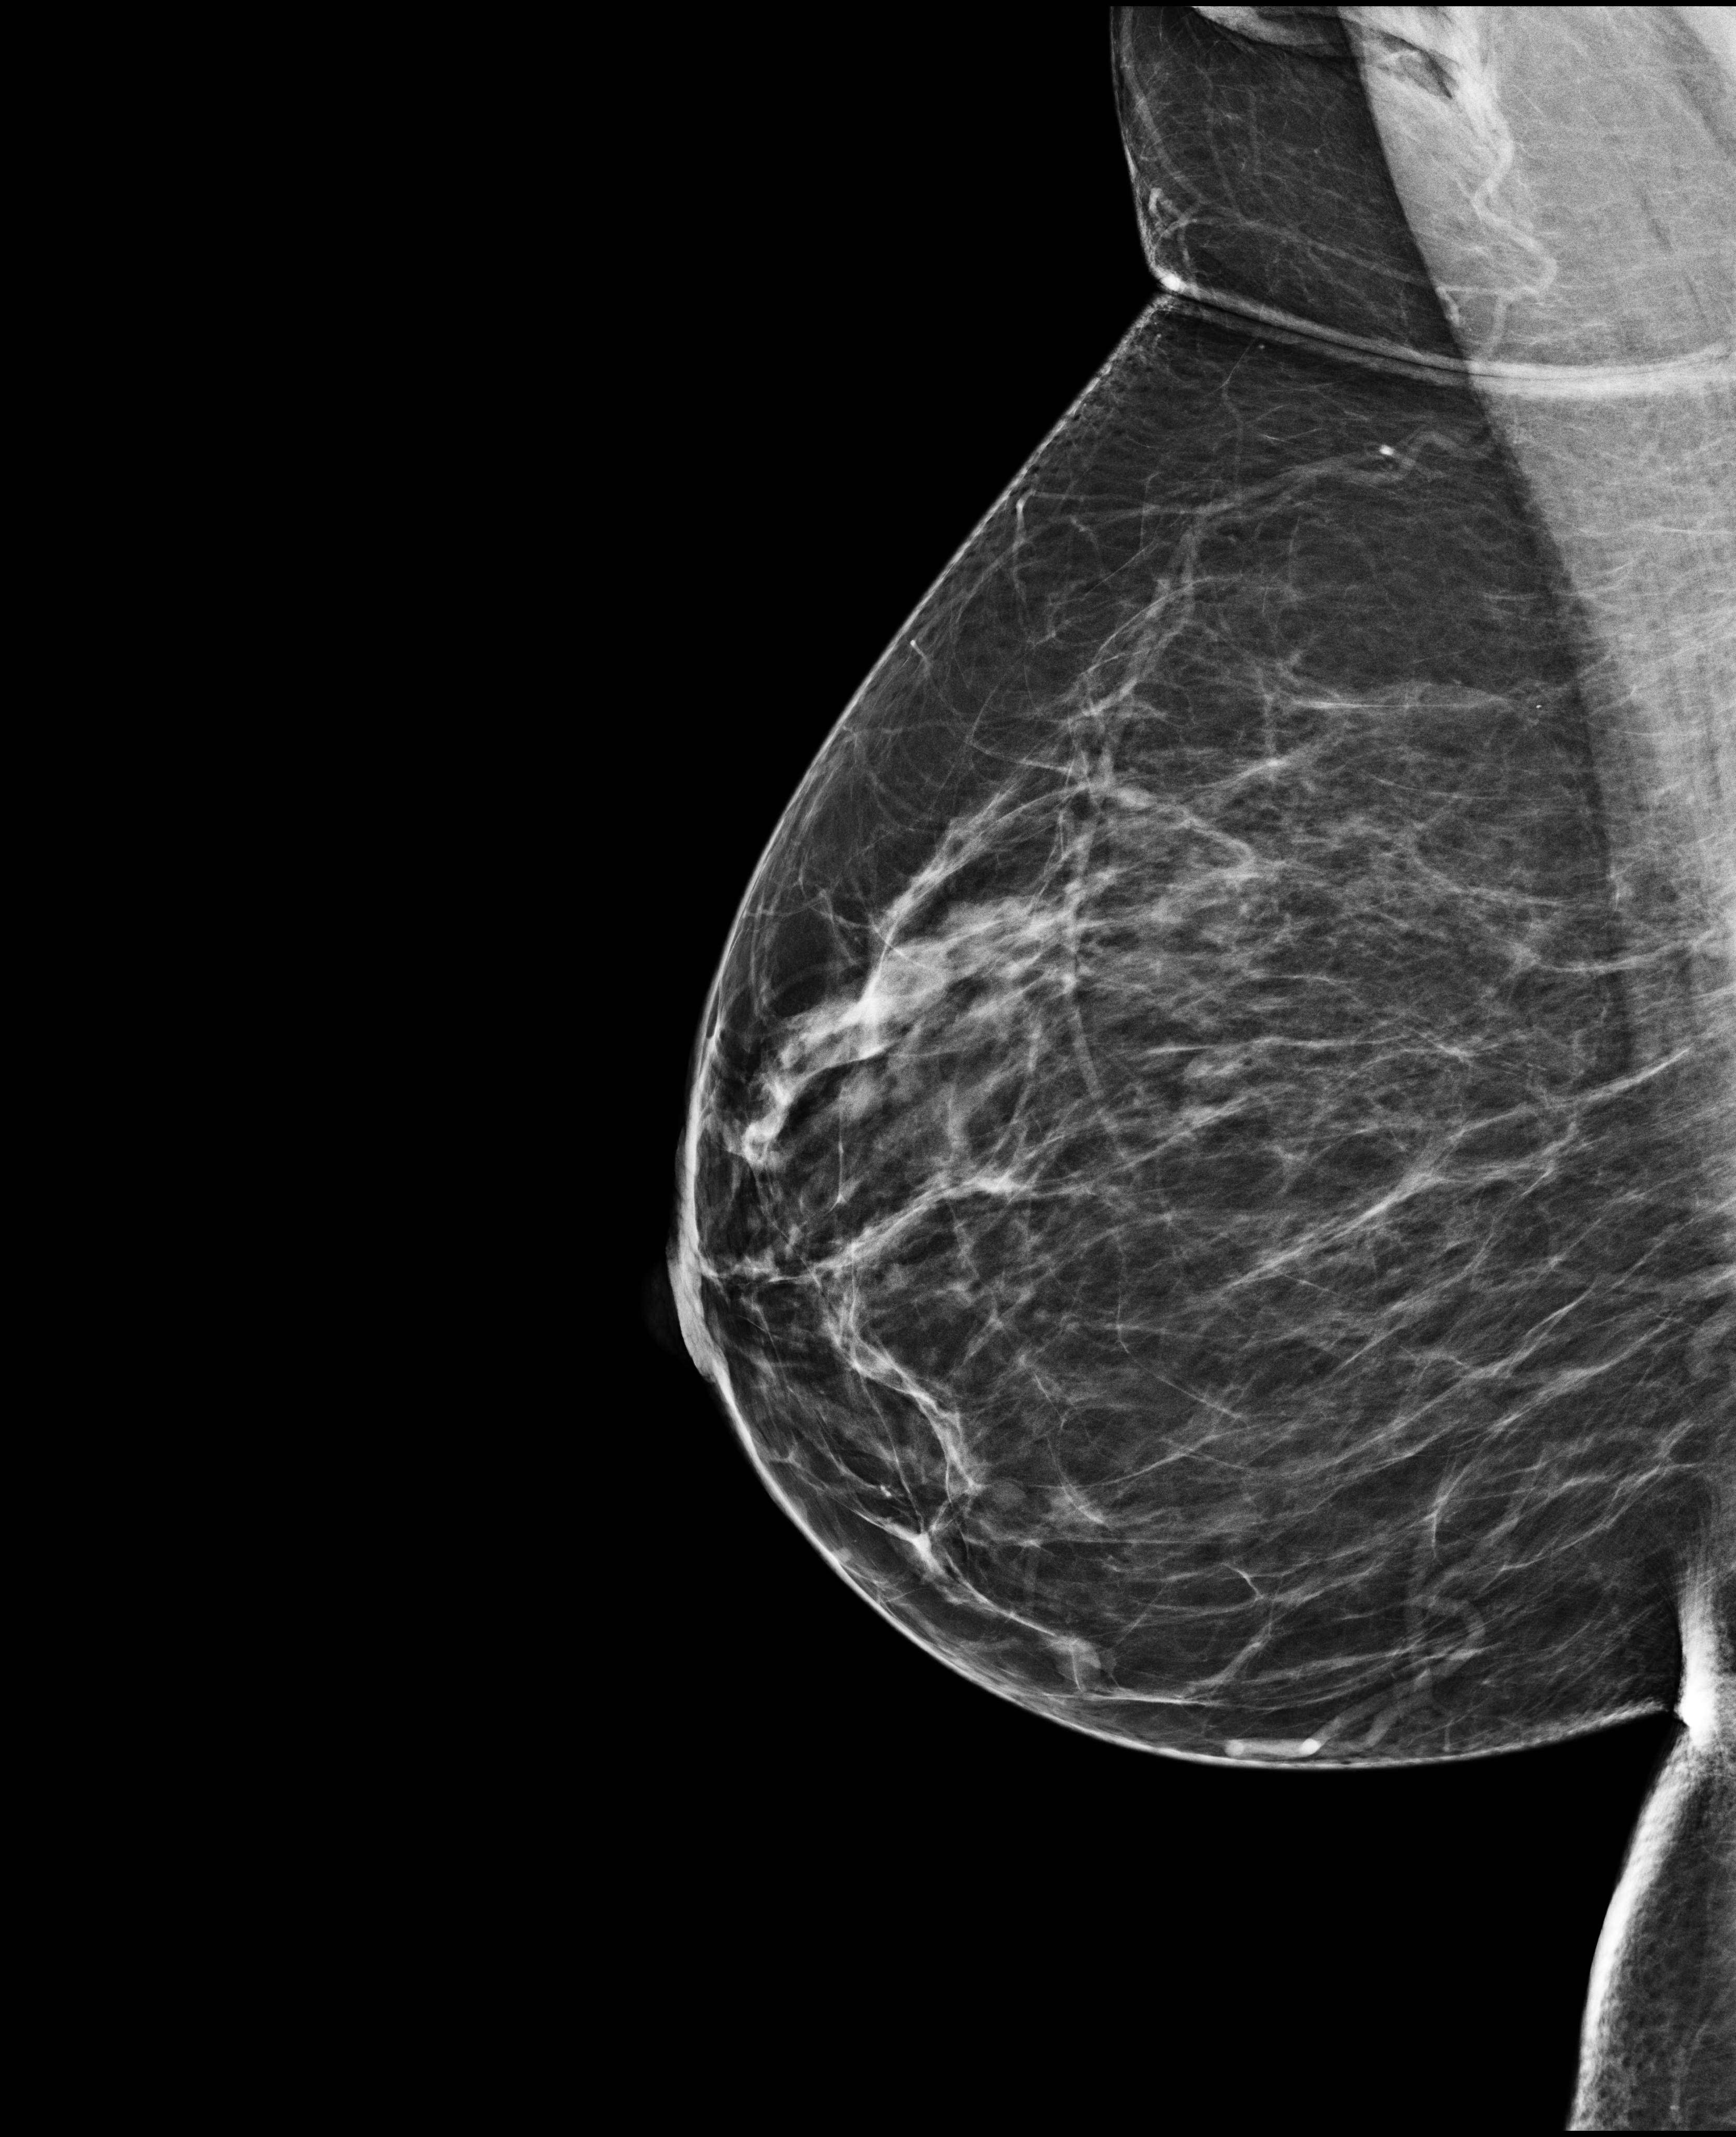
Full-field digital mammogram (FFDM); right breast; mediolateral oblique (MLO) view; screening examination. Patient: female, 64 years.
Breast density at the screening exam (both breasts): heterogeneously dense (BI-RADS density category c). Final BI-RADS assessment for this screening round (tomosynthesis exam, both breasts): category 2. Recall: no recall after this screen.